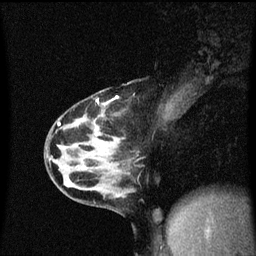
Breast MRI (dynamic contrast-enhanced), one sagittal slice; slice 23 of 60 in the series (ordered by position); dynamic contrast-enhanced series, image 2 of 3 at this slice position (ordered by acquisition); 1.5 T; TE 4.2 ms, TR 8.4 ms; 2 mm slice thickness; 256 × 256 image matrix. Patient: female, 32 years.
Structures marked on this image (semi-automatically segmented with operator editing):
- analysis volume of interest (the breast-tissue region the enhancement analysis was run in; not a lesion): bounding box [x1, y1, x2, y2] px = [55, 82, 169, 167]
- tumour enhancement mask (voxels above the 70 % enhancement threshold inside the analysis volume of interest): [117, 96, 119, 99]